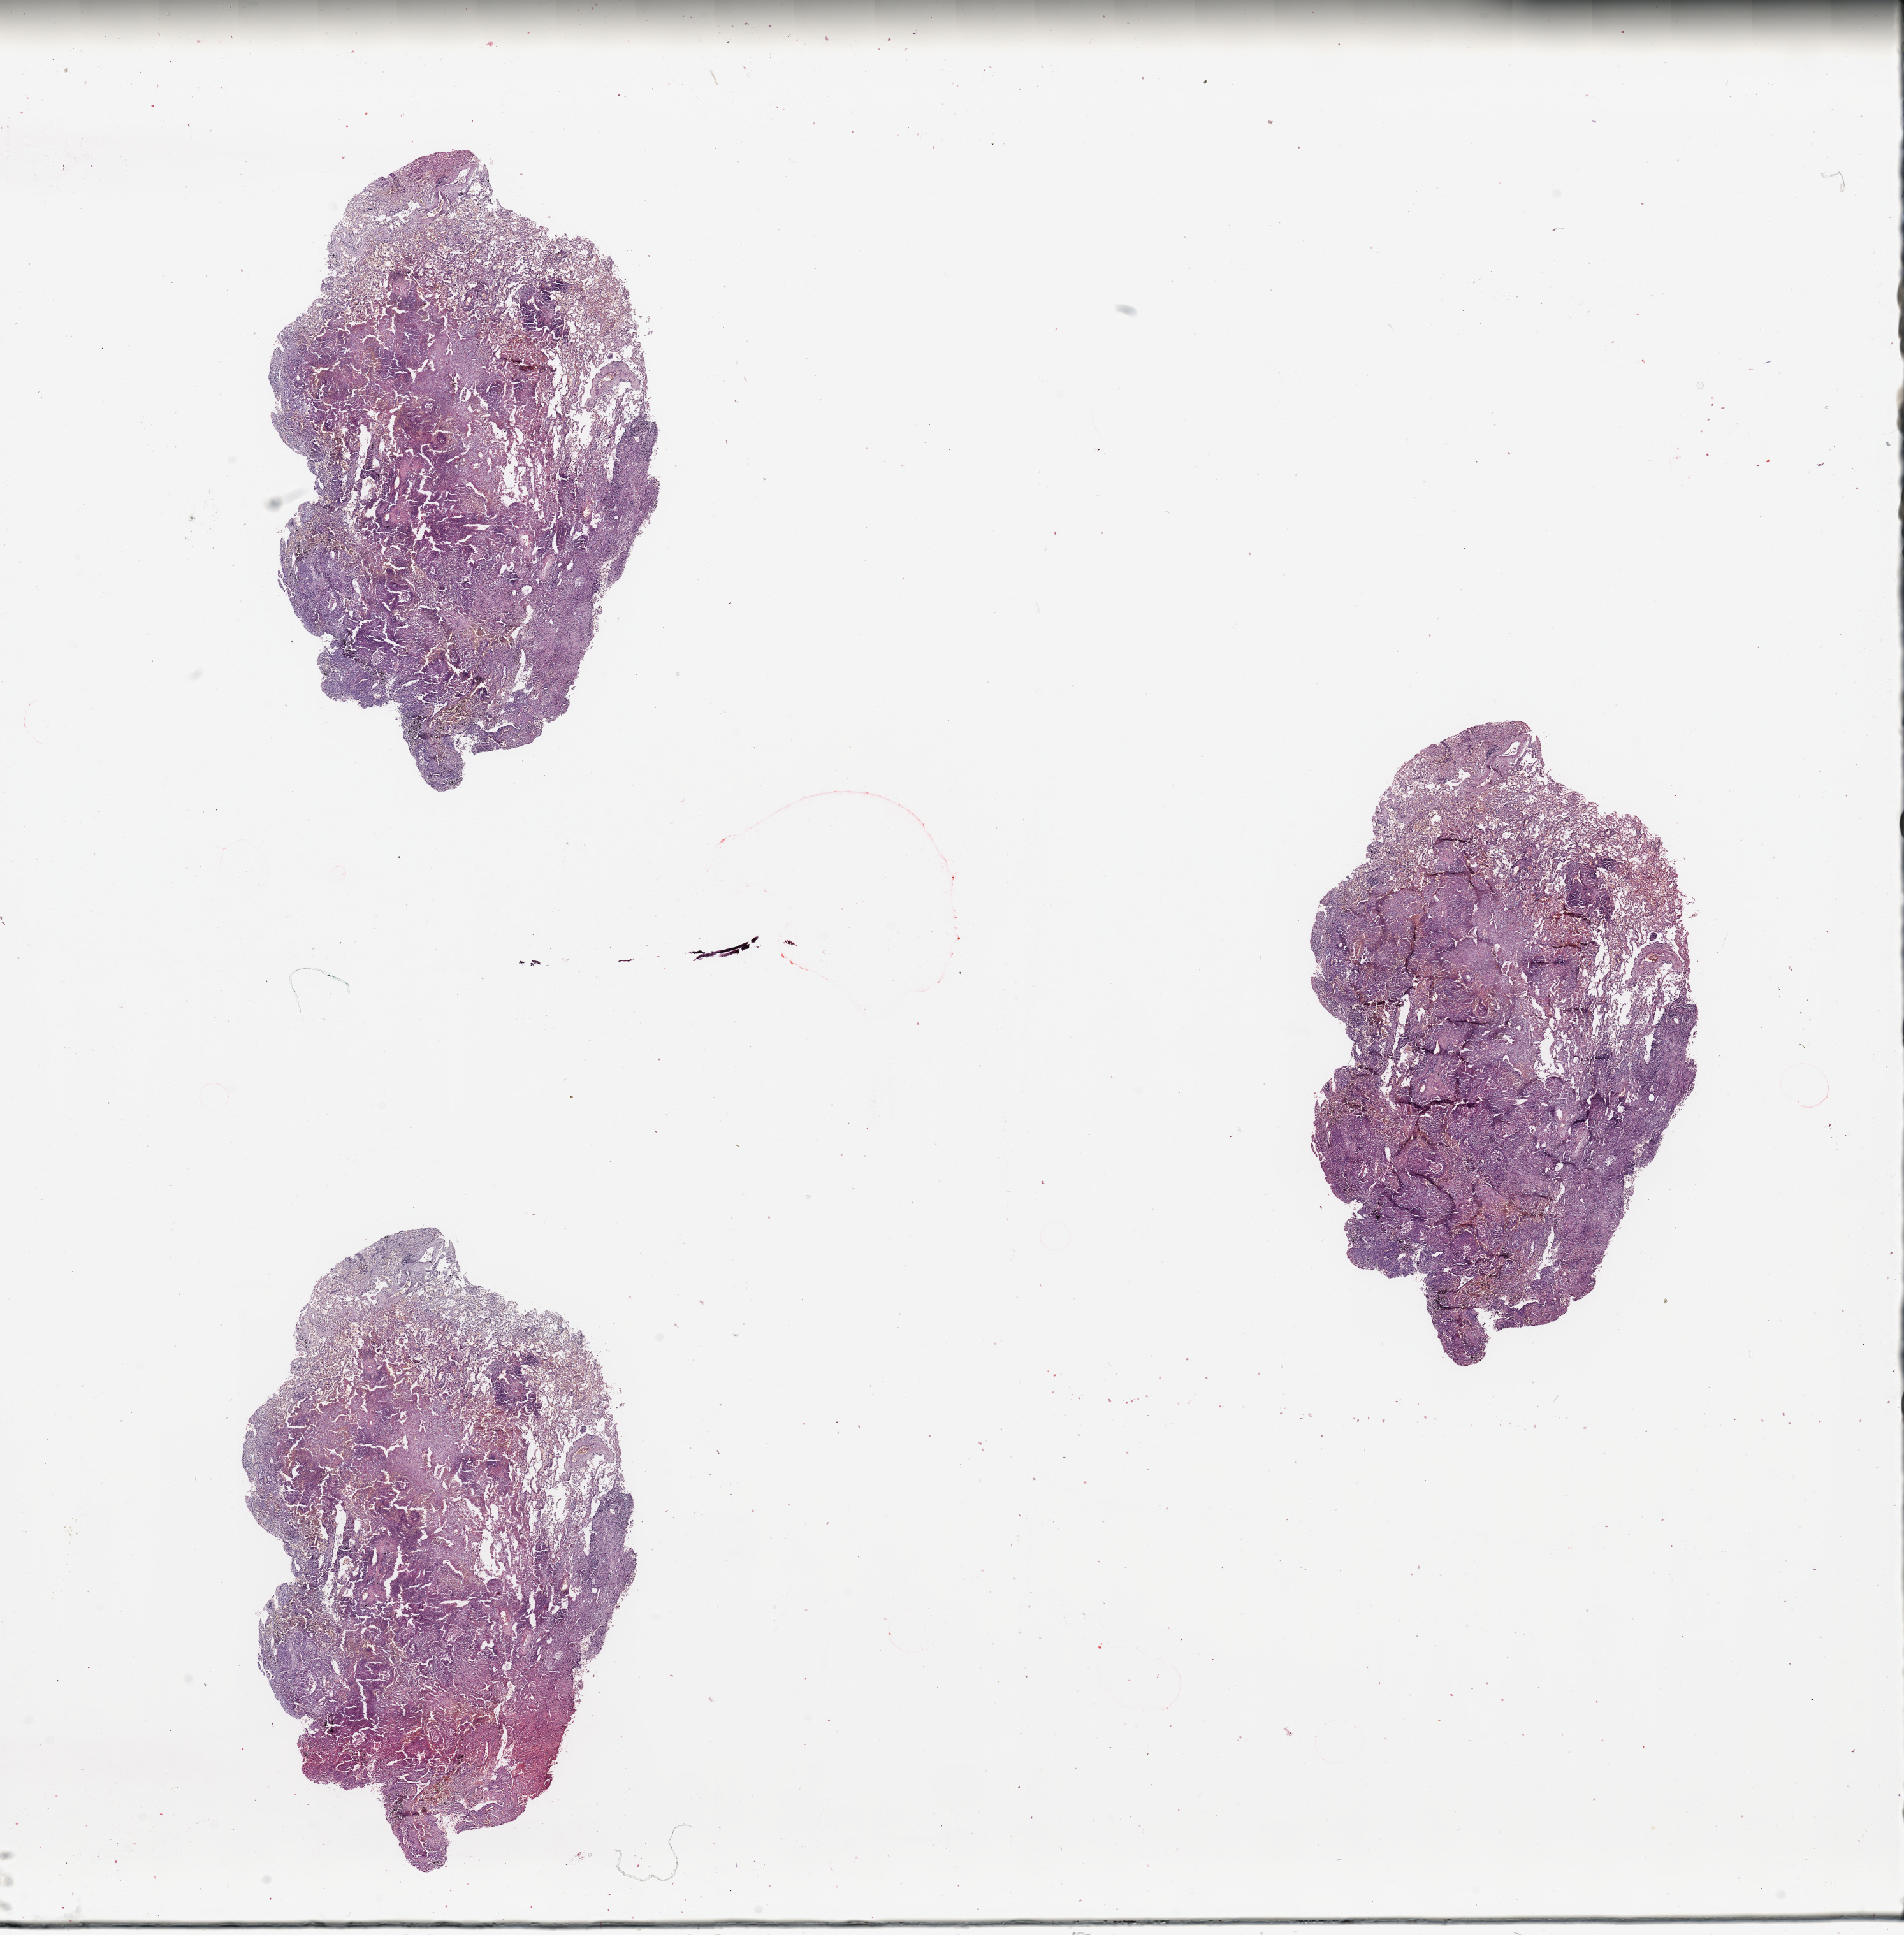
Digitized H&E tissue section (whole slide), whole scanned area (about 23.6 x 24.0 mm) shown as a low-resolution overview. Tumour tissue sample, sampled site: lung. 69-year-old male patient. Histologic grade: GX (grade cannot be assessed). Pathologist review of this section (percent, as recorded): tumour nuclei 55%, necrosis 10%.
- AJCC pathologic stage: IA
- histologic diagnosis: Adenocarcinoma, NOS
- primary tumour site (as recorded): left upper lobe